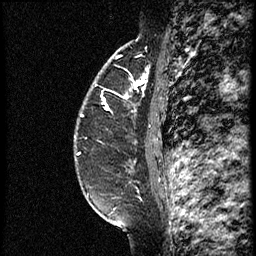
Breast MRI (dynamic contrast-enhanced), one sagittal slice; position 44 of 60 along the scan axis; dynamic contrast-enhanced study with each time point stored as its own series, time point 2 of 3 at this slice position (early post-contrast, ordered by acquisition time); 1.5 T; TE 4.2 ms, TR 18.9 ms; 2 mm slice thickness; 256 × 256 image matrix, field of view 200 × 200 mm. Female patient. From the clinical record (not read from this slice): setting: breast cancer imaged before/during neoadjuvant chemotherapy; receptor status: HER2-positive.
Outlined on this slice (semi-automatic segmentation, software-assisted and operator-edited):
- analysis volume of interest (the breast-tissue region the enhancement analysis was run in; not a lesion): bounding box (x1, y1, x2, y2) in pixels: (77, 64, 161, 147)
- tumour enhancement mask (voxels above the 100 % enhancement threshold inside the analysis volume of interest): (82, 81, 146, 118)